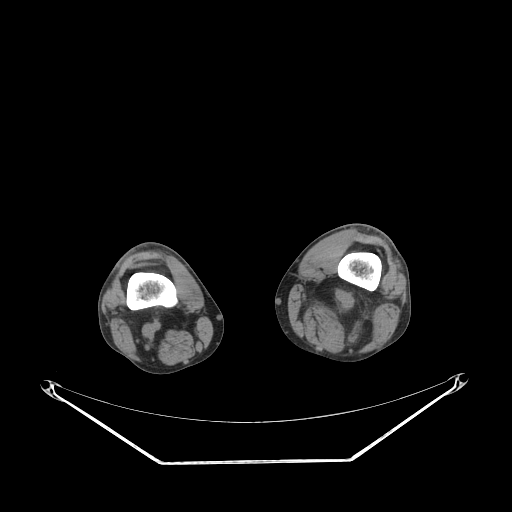
CT of an extremity soft-tissue mass (from a PET/CT study), one axial slice; position 199 of 267 along the scan axis; reconstruction kernel STANDARD; 140 kVp; soft-tissue window (W 400 / L 40 HU); 3.75 mm slice thickness; 512 × 512 image matrix, field of view 500 × 500 mm. Male patient. From the clinical record (not read from this slice): histological type: undifferentiated pleomorphic liposarcoma; grade: high; site of the primary tumour: left thigh.
Structures marked on this image (expert contour drawn on MRI and transferred to this co-registered scan by the dataset authors):
- gross tumour volume including surrounding oedema: bounding box <297,283,375,323> (left, top, right, bottom; pixels)